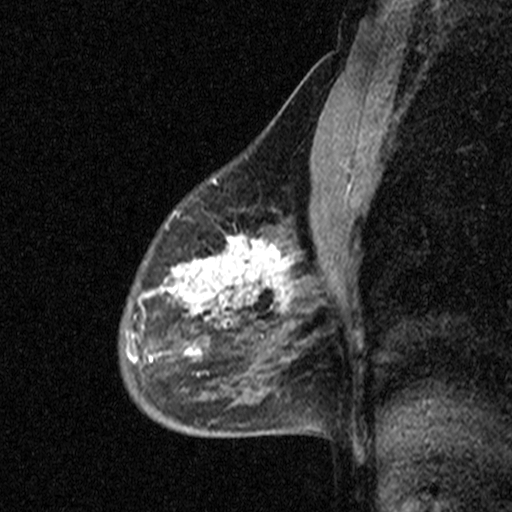
Breast MRI (dynamic contrast-enhanced), one sagittal slice; dynamic contrast-enhanced study with each time point stored as its own series, time point 2 of 3 at this slice position (early post-contrast, ordered by acquisition time); 1.5 T; TE 4.5 ms, TR 11 ms; 3 mm slice thickness; 512 × 512 image matrix, field of view 200 × 200 mm. Patient: female, 53 years. From the clinical record (not read from this slice): setting: breast cancer imaged before/during neoadjuvant chemotherapy; receptor status: HR-positive, HER2-negative.
Structures marked on this image (semi-automatic segmentation, software-assisted and operator-edited):
- analysis volume of interest (the breast-tissue region the enhancement analysis was run in; not a lesion): bounding box (x1, y1, x2, y2) in pixels: (88, 176, 313, 423)
- tumour enhancement mask (voxels above the 90 % enhancement threshold inside the analysis volume of interest): (128, 226, 289, 374)